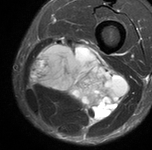
MRI of an extremity soft-tissue mass, one axial slice; slice 36 of 90 in the series (ordered by position); STIR; MR volume resampled by the dataset authors to the PET/CT grid (not the native acquisition matrix); 152 × 150 image matrix. Male patient. From the clinical record (not read from this slice): histological type: undifferentiated pleomorphic liposarcoma; grade: high; site of the primary tumour: left thigh.
Structures marked on this image (expert contour drawn on MRI and transferred to this co-registered scan by the dataset authors):
- gross tumour volume including surrounding oedema: bounding box (x1, y1, x2, y2) in pixels: (32, 37, 126, 124)
- gross tumour volume (mass): (36, 48, 122, 118)